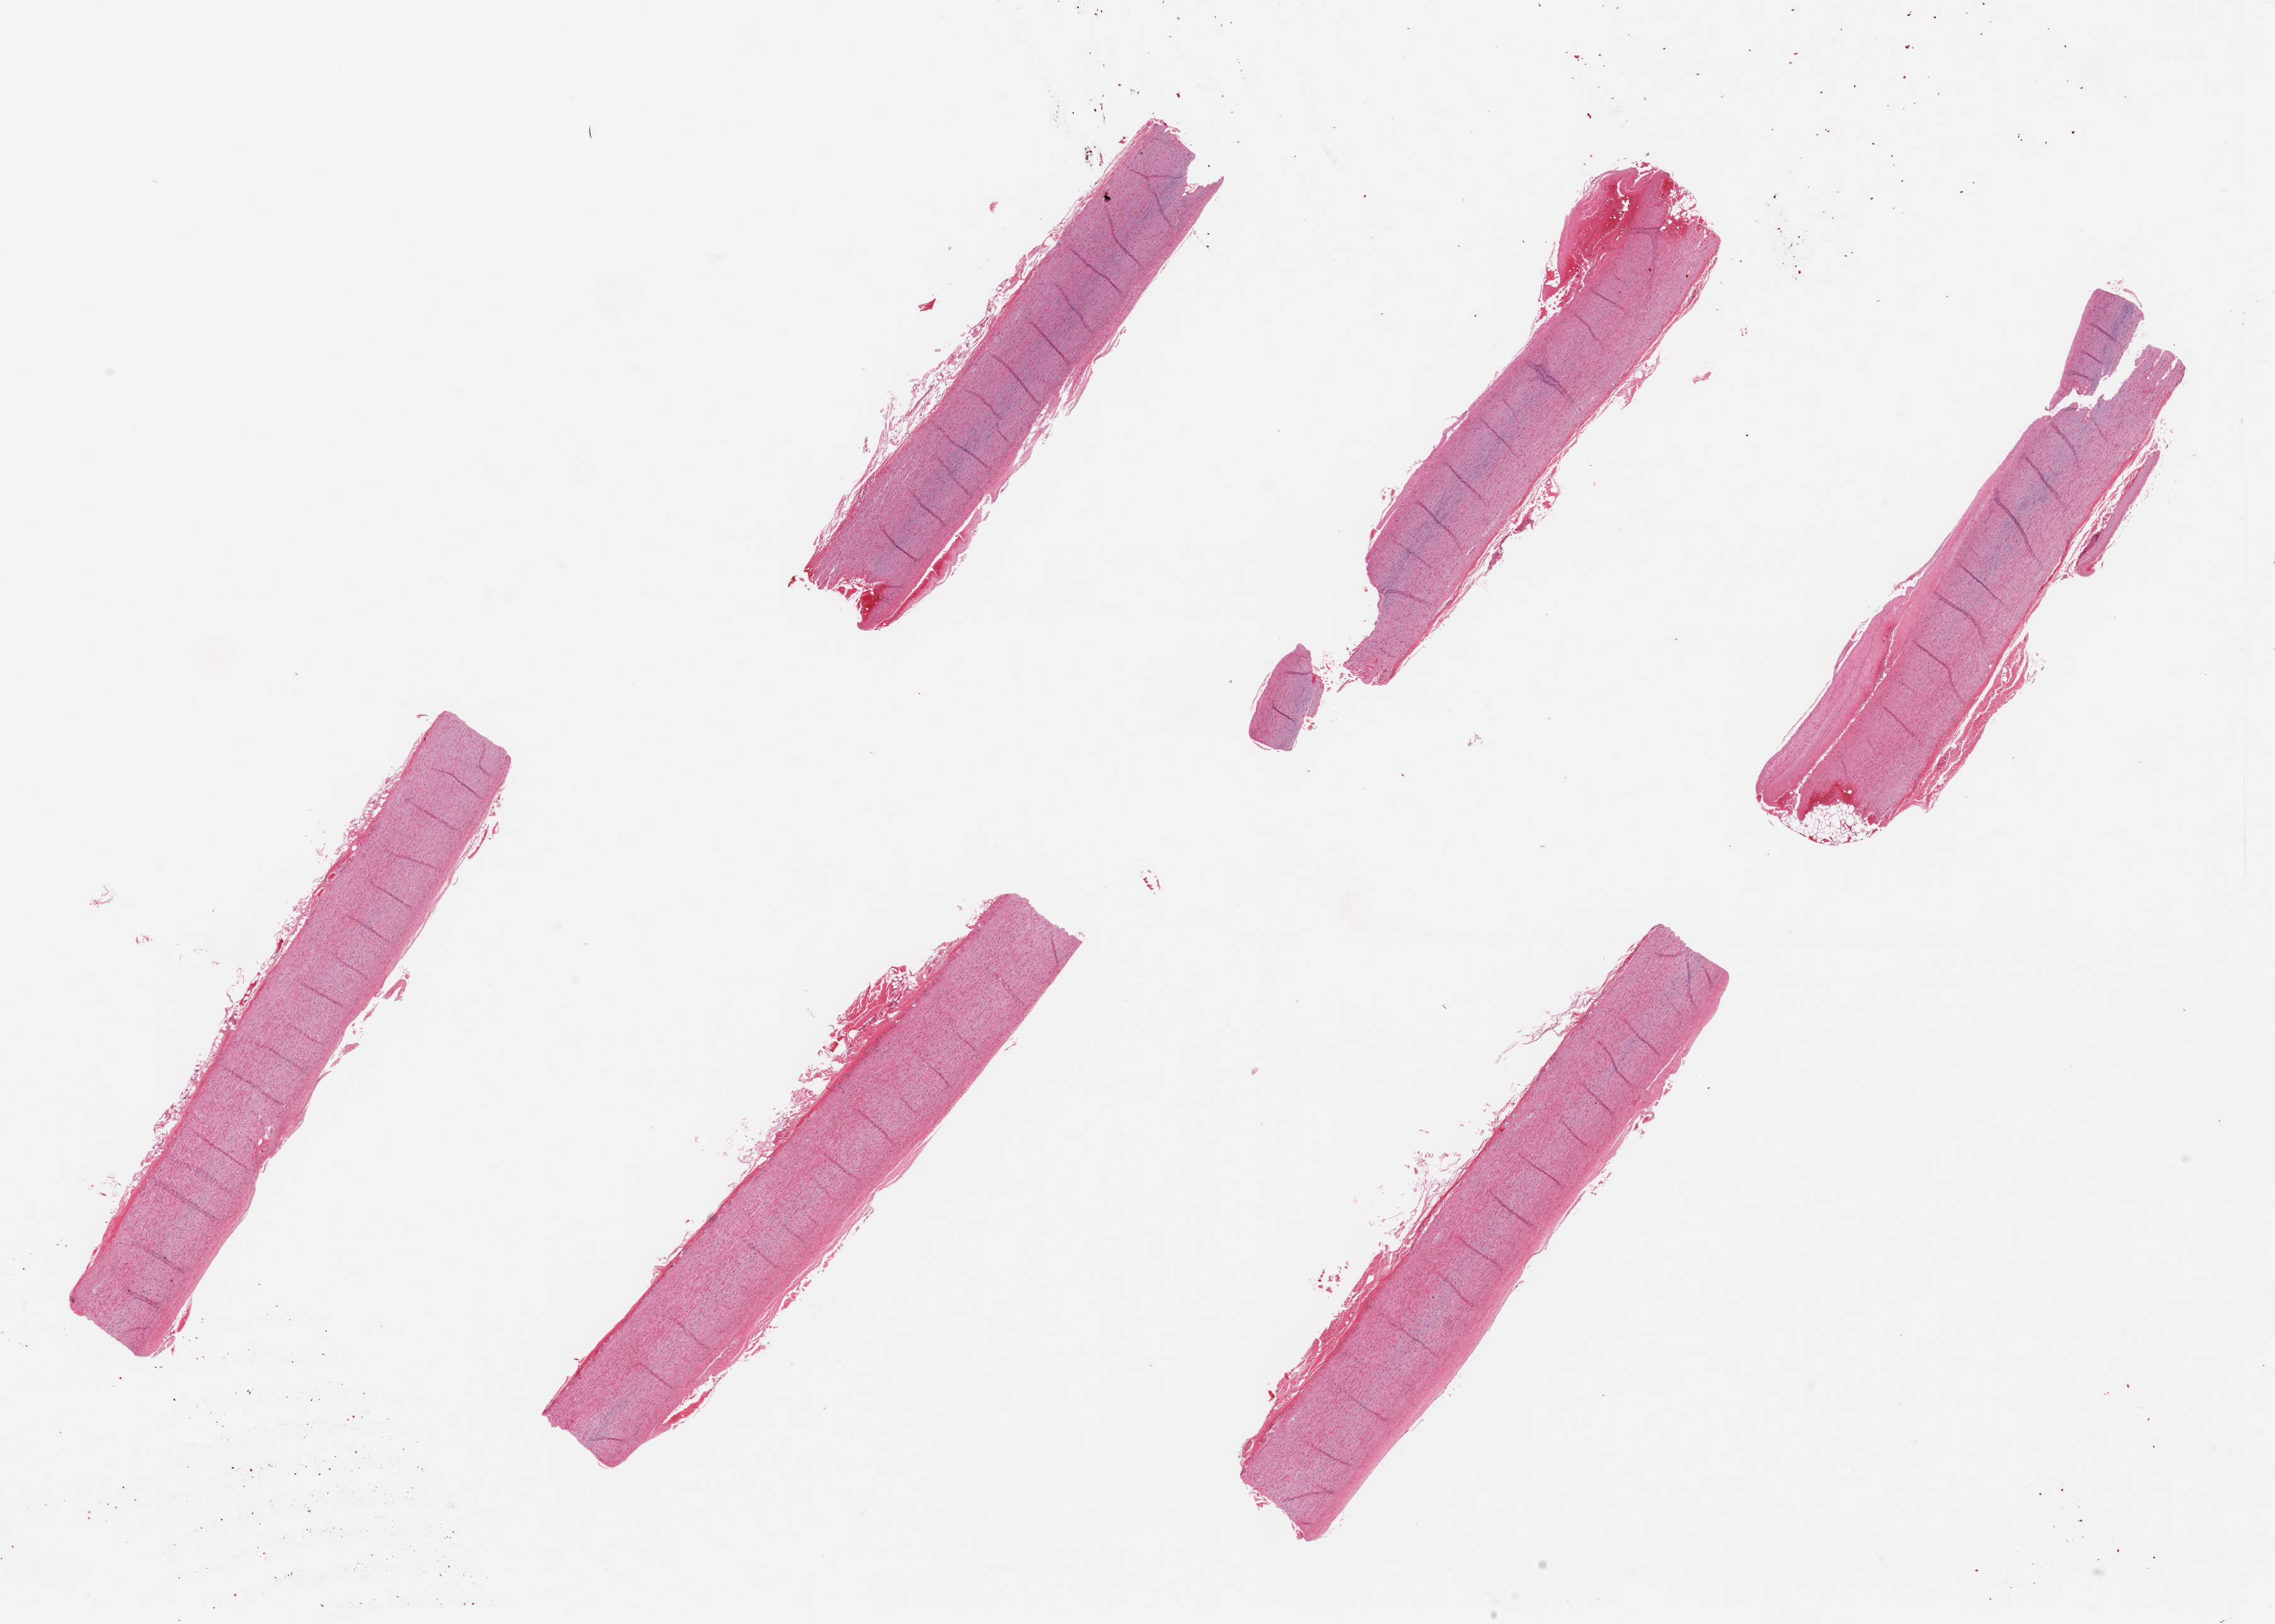
H&E whole-slide image, brightfield, shown as a low-resolution overview of the whole scanned area (about 28.5 x 20.4 mm). PAXgene-fixed, paraffin-embedded tissue. Section of aorta (target tissue). Tissue donor sample. Donor: male.
• pathologist's review note for this sample: 6 pieces, up to 9x2mm; mural hemorrhage, probably traumatic